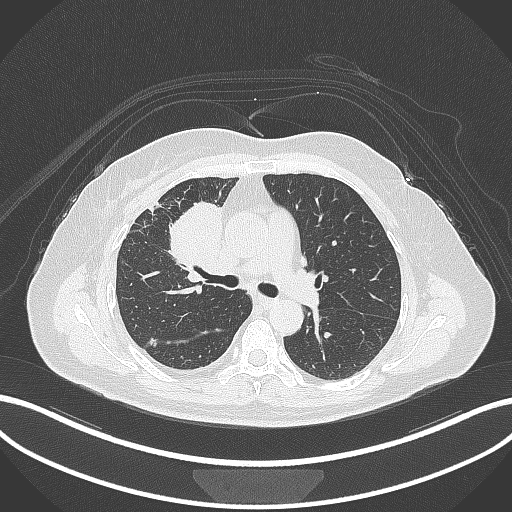
Chest CT, one axial slice. Position 172 of 305 along the scan axis. Lung window (W 1500 / L -600 HU). 512 × 512 image matrix, field of view 400 × 400 mm. Patient: female, 52 years. Case-level facts recorded for this patient, not image findings: clinical TNM (as recorded): T3 N1 M1.
Annotated regions visible in this slice (rectangle marked by the reading radiologist):
- lung tumour (recorded histology: adenocarcinoma): bounding box (x1, y1, x2, y2) in pixels: (166, 201, 225, 278)